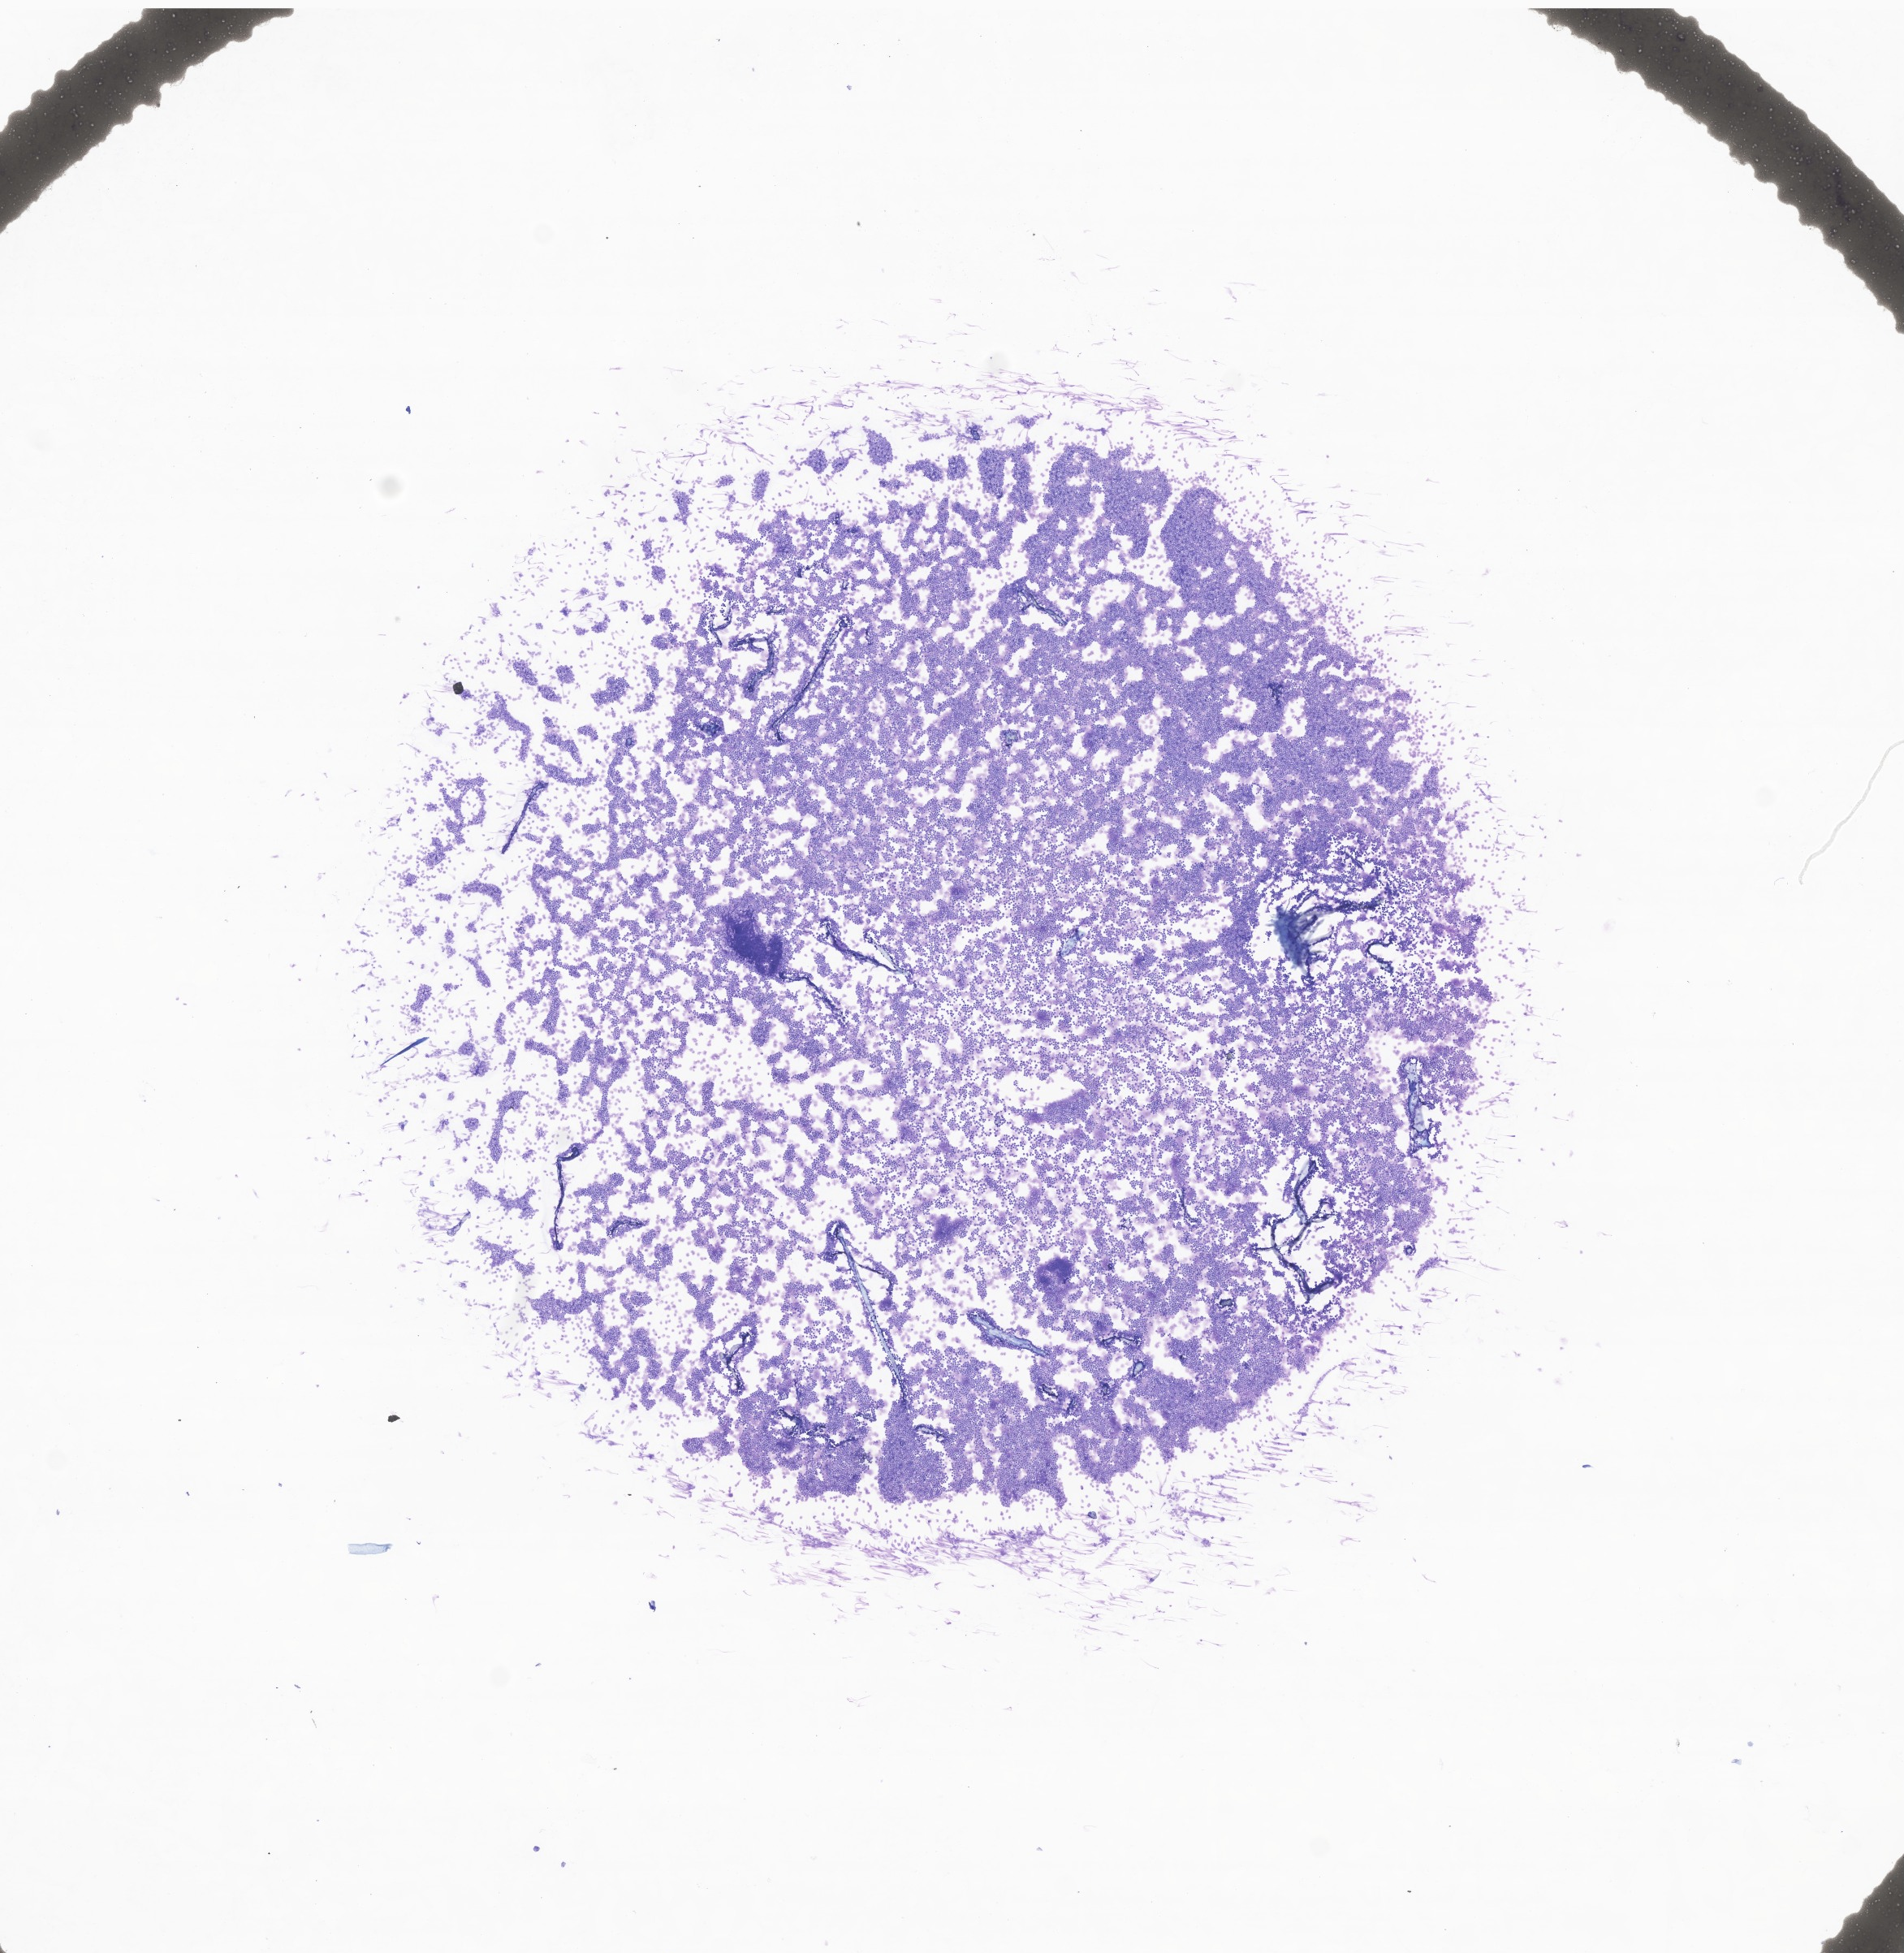
Whole-slide image of tumor tissue from the adrenal gland — low-resolution overview of the scanned area, about 9.9 x 10.1 mm. Patient male; age 91 months (7 years 7 months).
- tissue or organ of origin (case record): retroperitoneum
- diagnosis (ICD-O-3 morphology term): Neuroblastoma, NOS